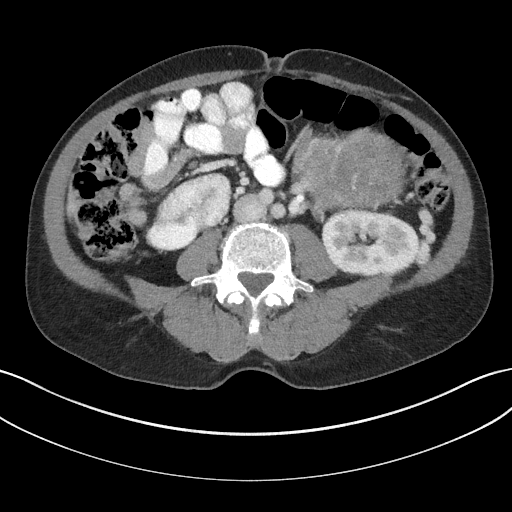
Contrast-enhanced abdominal CT, one axial slice. Position 75 of 147 along the scan axis. Intravenous contrast given. Soft-tissue window (W 400 / L 40 HU). 512 × 512 image matrix, field of view 384 × 384 mm. Patient: male, 58 years. From the clinical record (not read from this slice): diagnosis: adrenocortical carcinoma; tumour side: left adrenal; tumour size at pathology: 22 cm.
Outlined on this slice (semi-automatically segmented with operator editing):
- mass: bounding box [x1, y1, x2, y2] px = [299, 131, 403, 208]